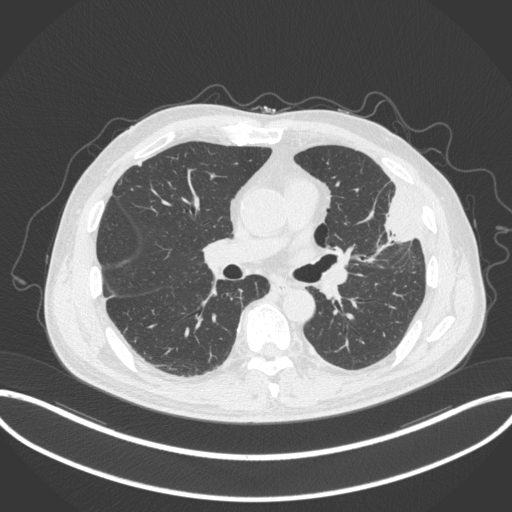
Chest CT, one axial slice; slice 183 of 382 in the series (ordered by position); reconstruction kernel B31f; lung window (W 1500 / L -600 HU); 512 × 512 image matrix, field of view 415 × 415 mm. Patient: male, 64 years. Case-level facts recorded for this patient, not image findings: clinical TNM (as recorded): T4 N1 M0.
Annotated regions visible in this slice (rectangle marked by the reading radiologist):
- lung tumour (recorded histology: adenocarcinoma): box from (x=374, y=186) to (x=420, y=248) px